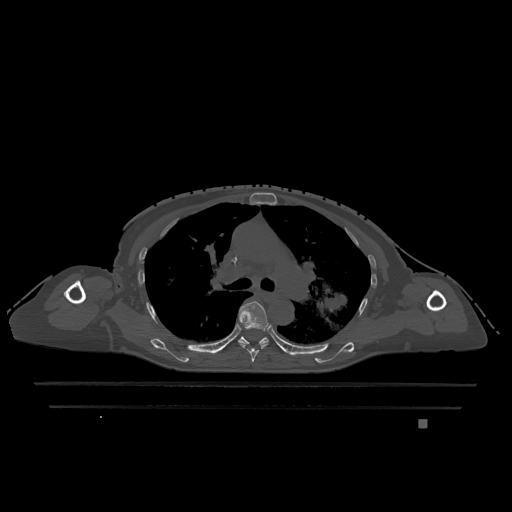
CT including the spine, one axial slice. Slice 816 of 1317 in the series (ordered by position). Bone window (W 1800 / L 400 HU). 0.5 mm slice thickness. 512 × 512 image matrix. Female patient, age 74 years. From the clinical record (not read from this slice): primary cancer: lung; vertebrae with lytic lesions (as recorded): T1, T4, T5, T6, L4, L5.
Structures marked on this image (semi-automatic segmentation, software-assisted and operator-edited):
- T5 vertebra: bounding box [x1, y1, x2, y2] px = [238, 301, 269, 362]
- T6 vertebra: [238, 336, 269, 344]